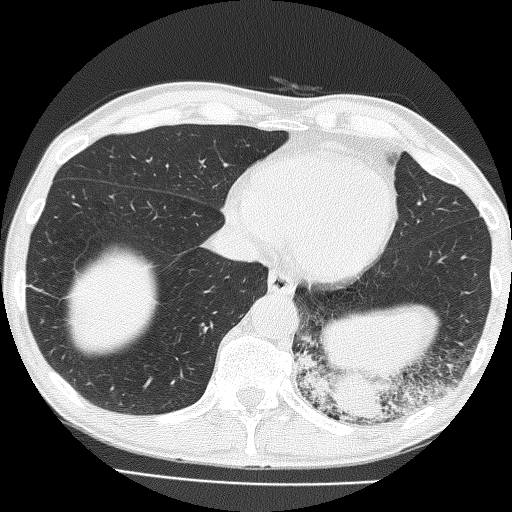
Chest CT (low-dose screening protocol), one axial image. First (baseline) screen. Lung window (W 1500 / L -600 HU). 2 mm slice thickness. Lung (sharp) reconstruction kernel (FC51). 120 kVp. Slice 112 of 160 in the series. 512 × 512 image matrix. Male, age 58 years at enrolment. Current smoker at enrolment.
Lesion marked by an expert reader, box from (x=288, y=291) to (x=431, y=435) px. The screening reader recorded 2 non-calcified nodules or masses ≥4 mm on this exam (left lower lobe, left upper lobe); which of them this box marks is not recorded. Later outcome: lung cancer diagnosed 39 days after this screen — non-small cell carcinoma, left lower lobe, poorly differentiated (G3), stage IV (AJCC 6th edition), 74 mm at pathology.